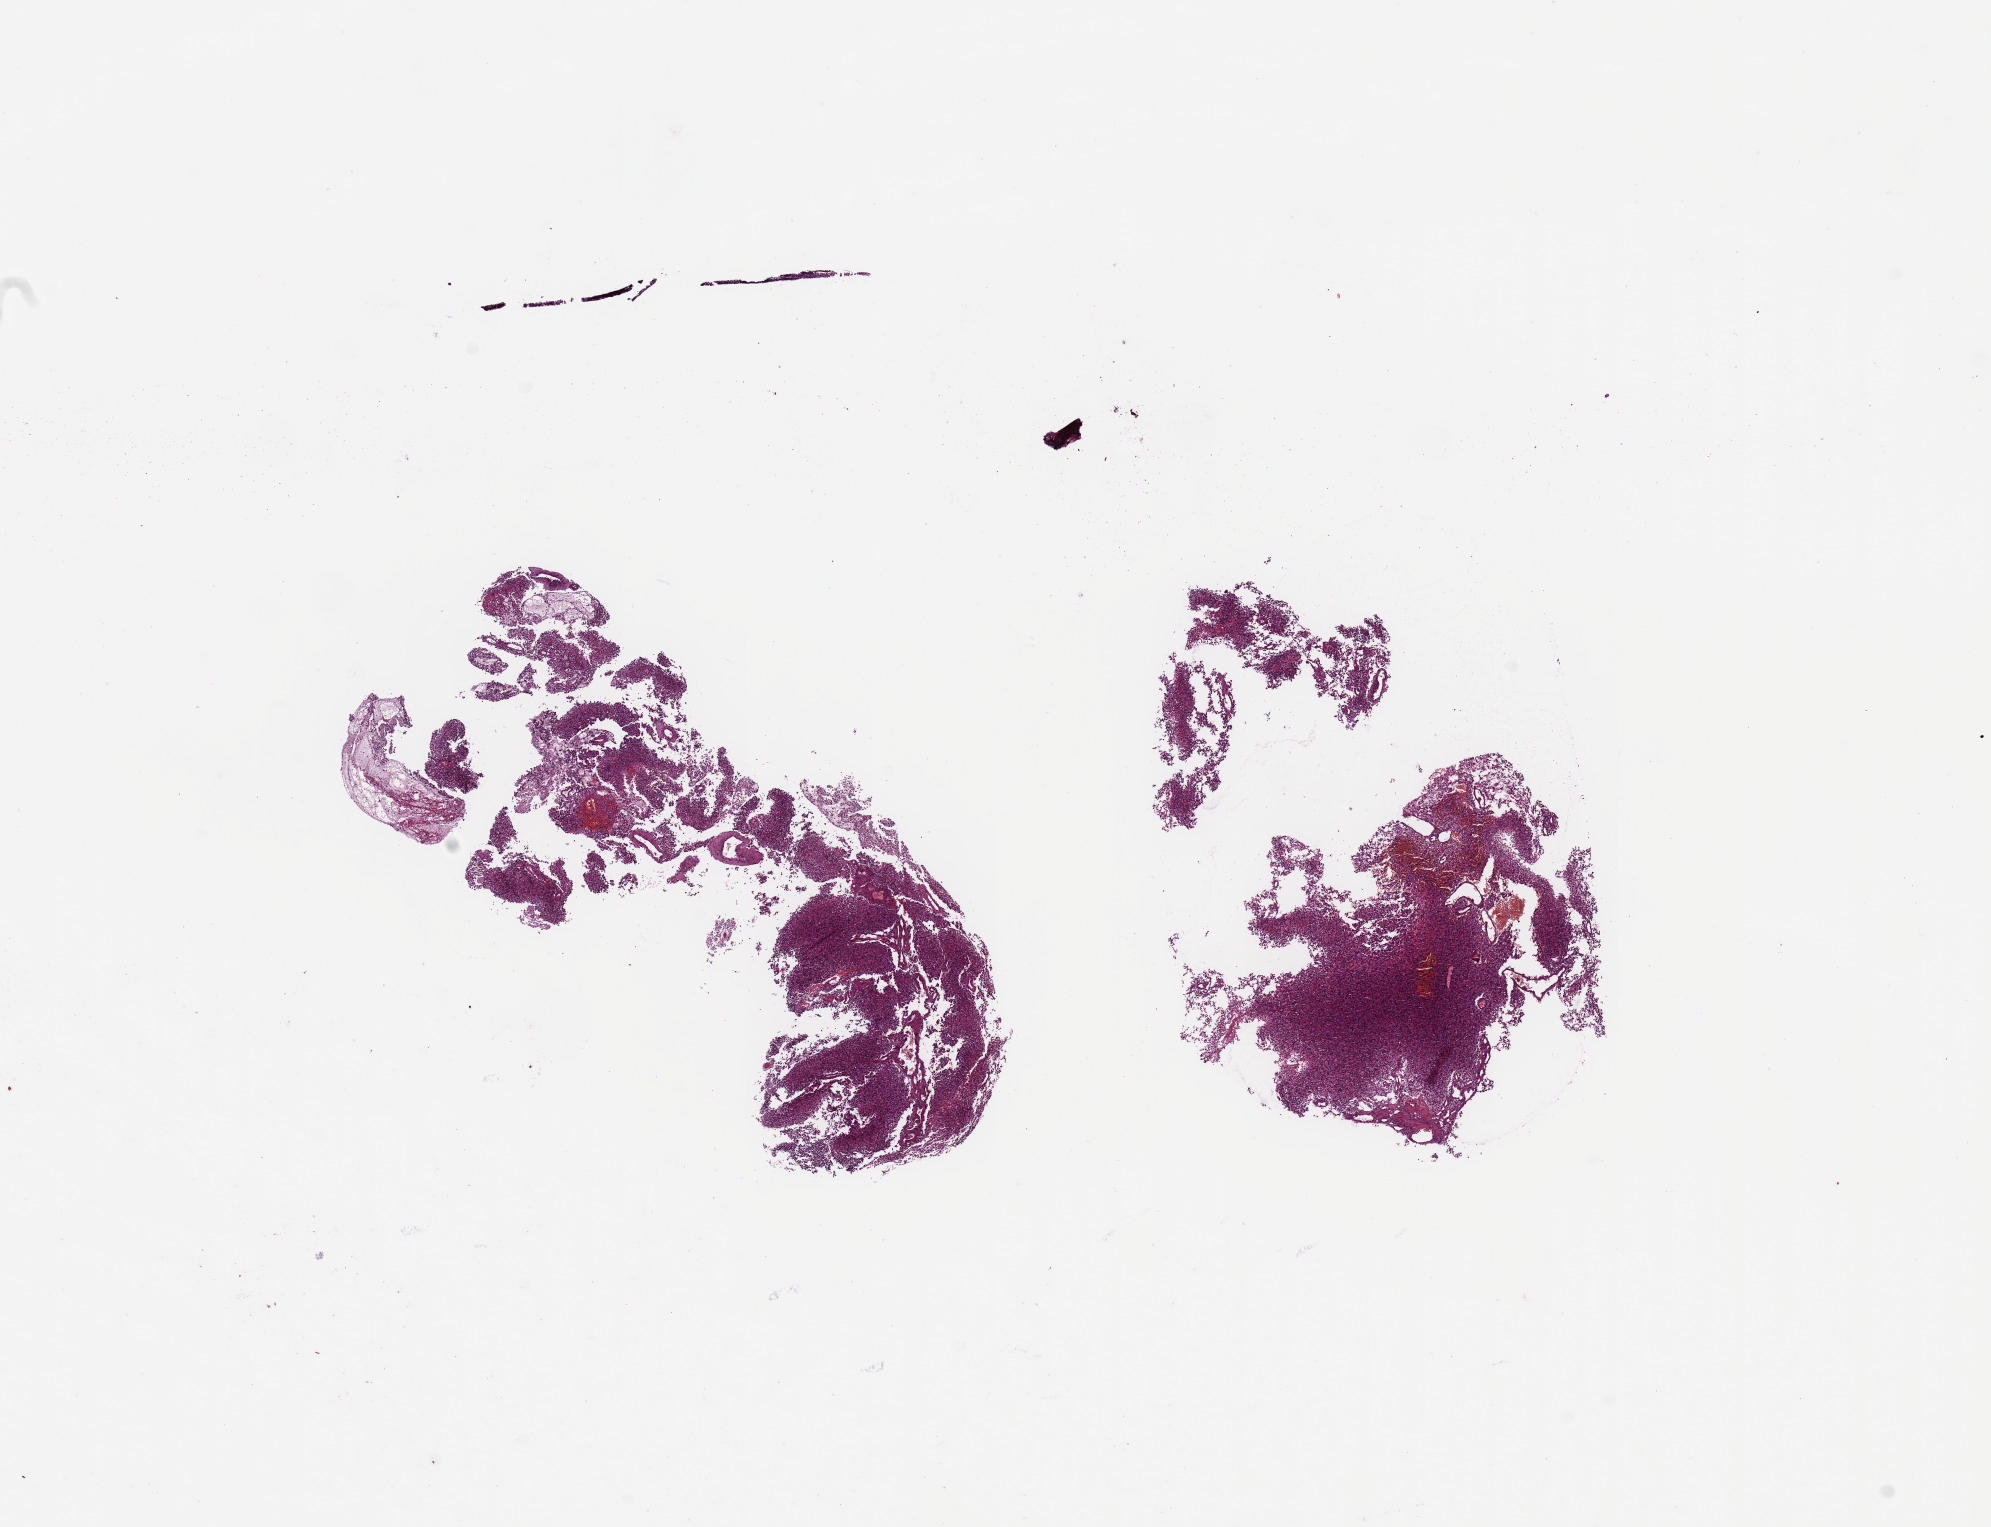
Whole-slide histology image, H&E — whole scanned area (about 15.8 x 12.1 mm) shown as a low-resolution overview, tumour tissue sample, sampled site: brain. Female, 47 y/o. Slide review estimates, as recorded: tumour nuclei 80%, necrosis 5%.
Diagnosis: Glioblastoma.